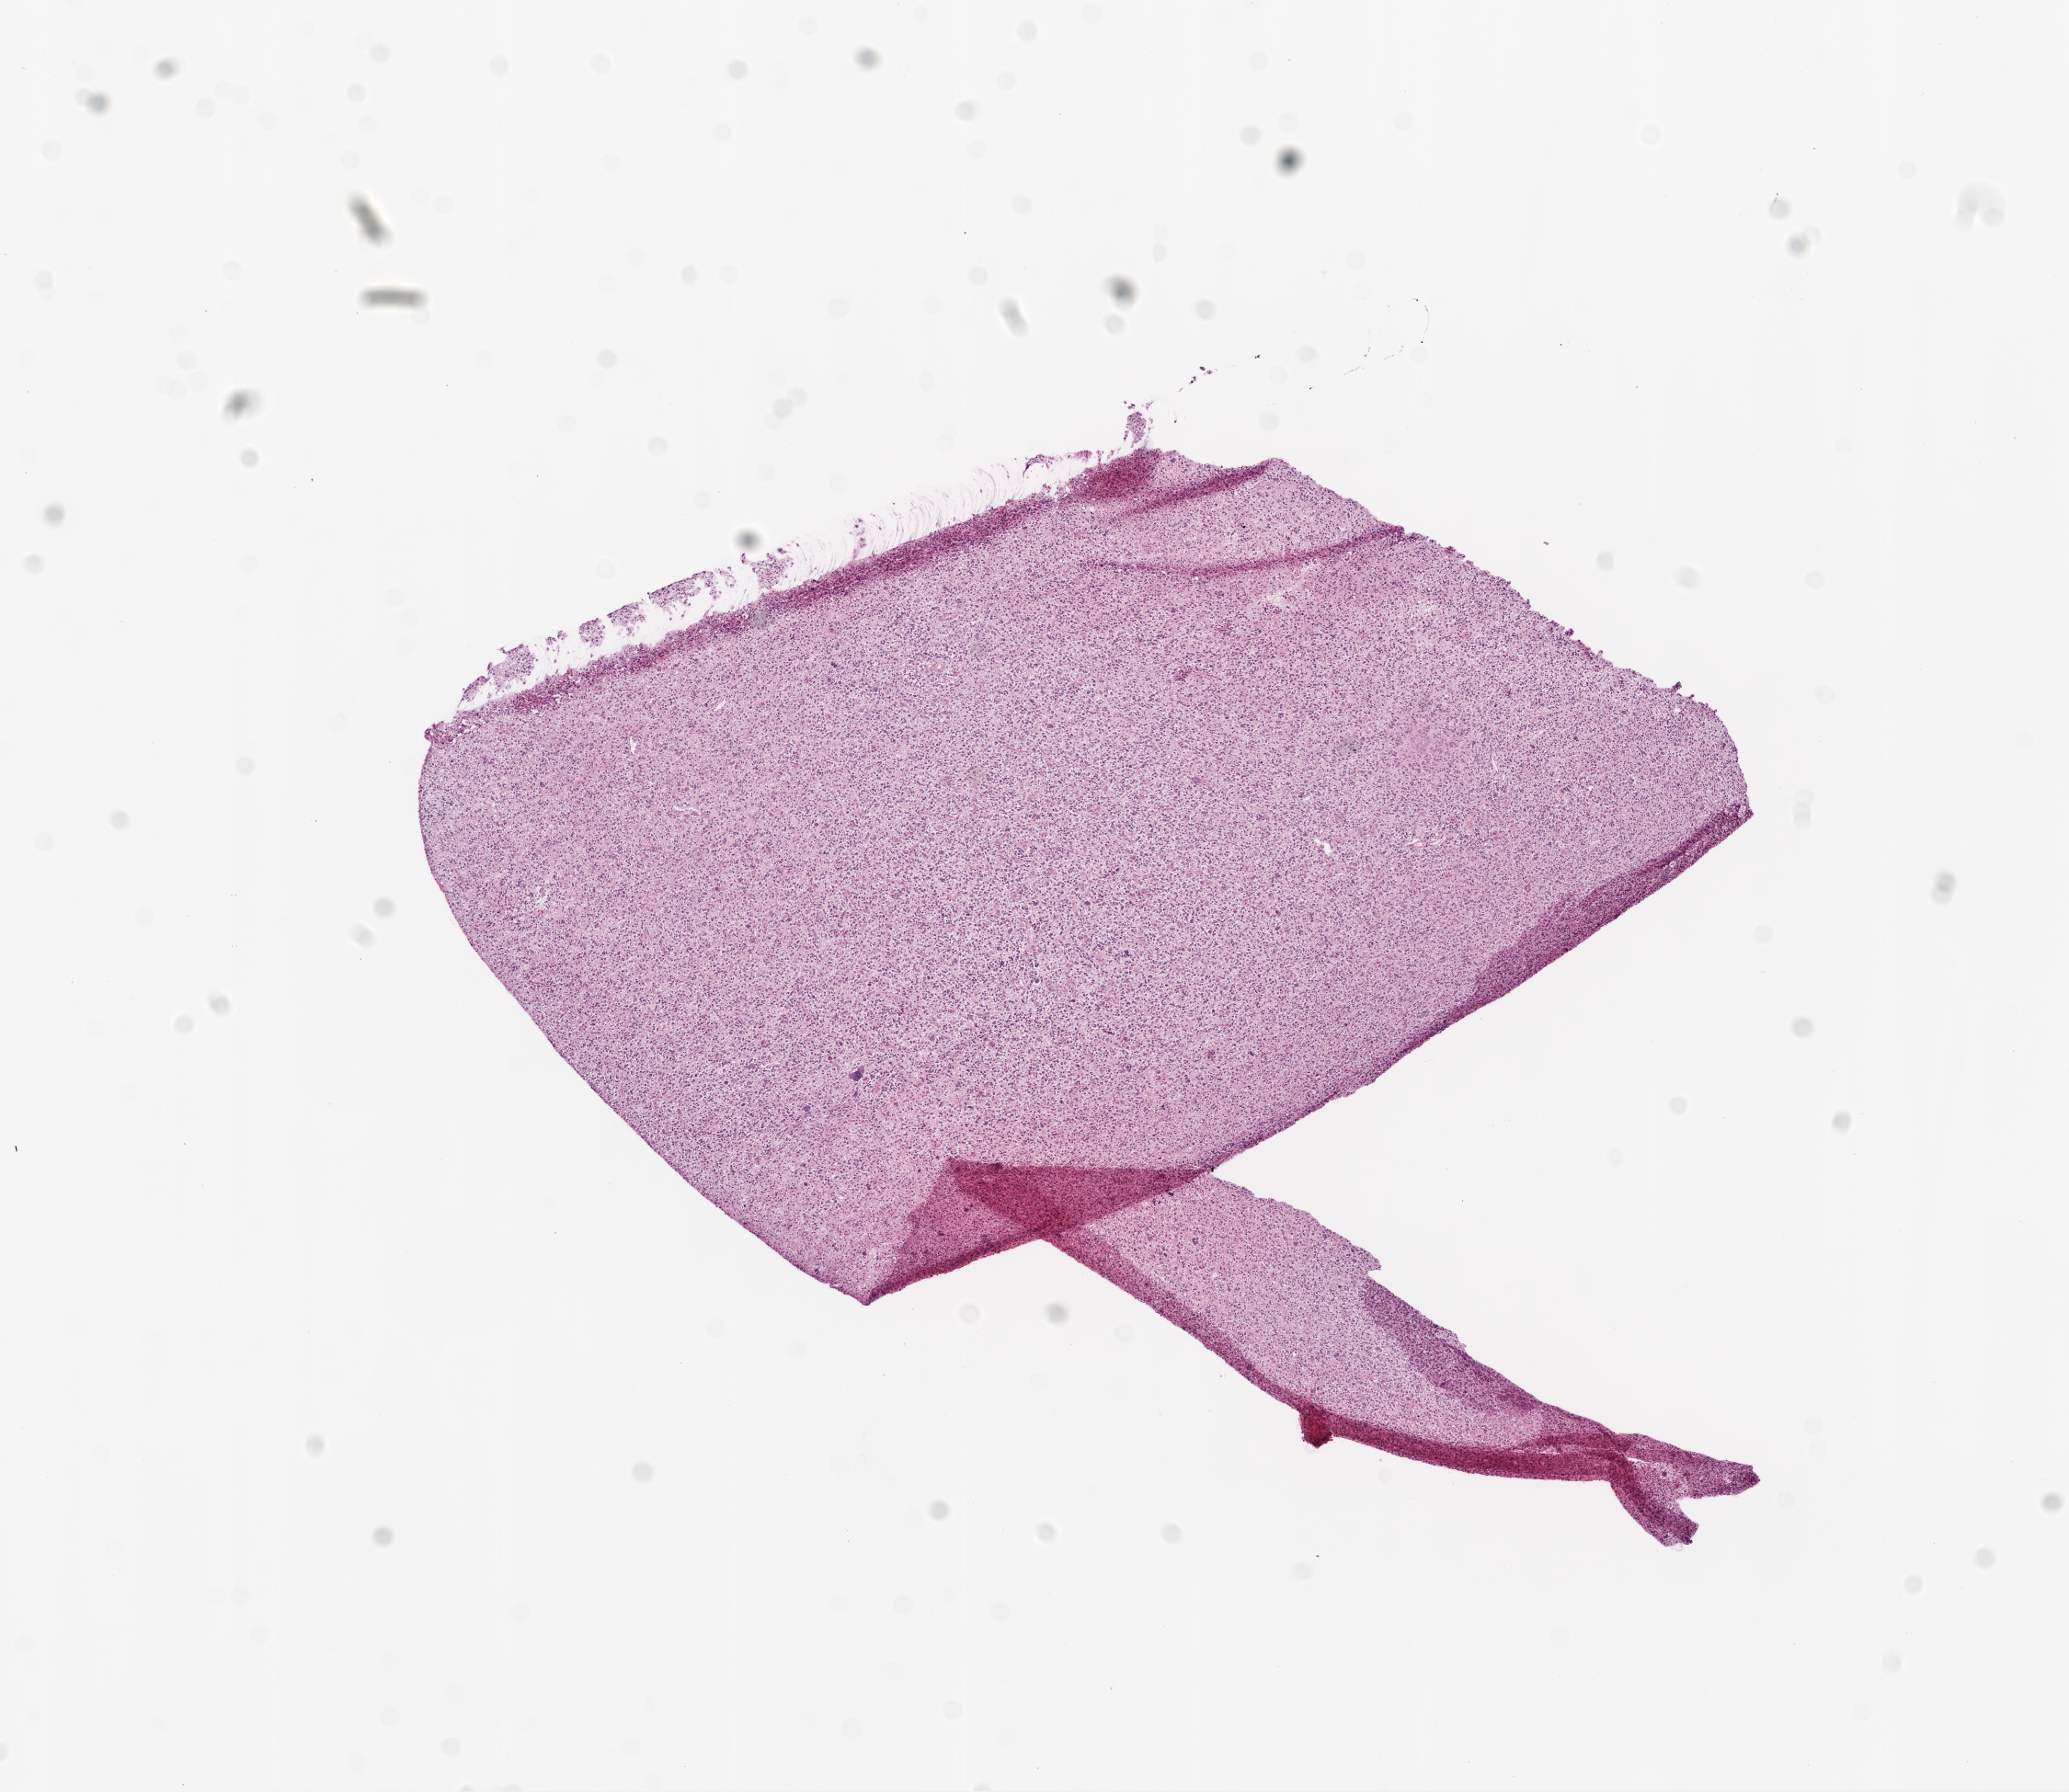
Digitized H&E-stained tissue section (whole slide), a low-resolution overview of the entire scanned area, about 9.0 x 7.8 mm. Frozen section. Brain, primary tumour sample. Patient: male, age at initial diagnosis 59 years. Slide review estimates, as recorded: tumour cells 100%, tumour nuclei 90%, normal cells 0%, stromal cells 0%, necrosis 0%.
Pathologic diagnosis: Glioblastoma.